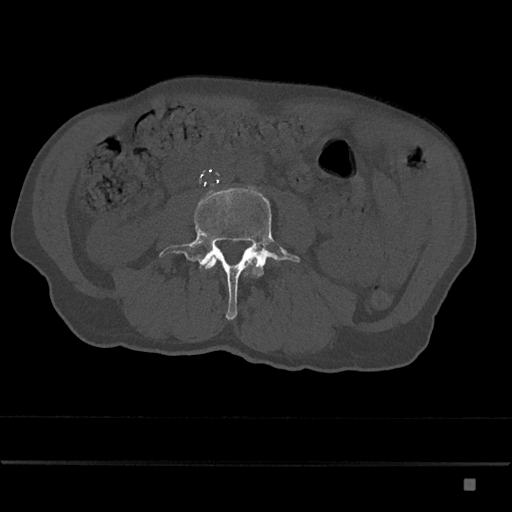
CT including the spine, one axial slice. Slice 350 of 797 in the series (ordered by position). Reconstruction kernel Br40s/3. 120 kVp. Bone window (W 1800 / L 400 HU). 0.5 mm slice thickness. 512 × 512 image matrix, field of view 390 × 390 mm. Patient: male, 72 years. From the clinical record (not read from this slice): primary cancer: prostate.
Annotated regions visible in this slice (semi-automatic segmentation, software-assisted and operator-edited):
- L3 vertebra: box from (x=205, y=257) to (x=255, y=269) px
- L4 vertebra: (x=159, y=188)–(x=301, y=320)